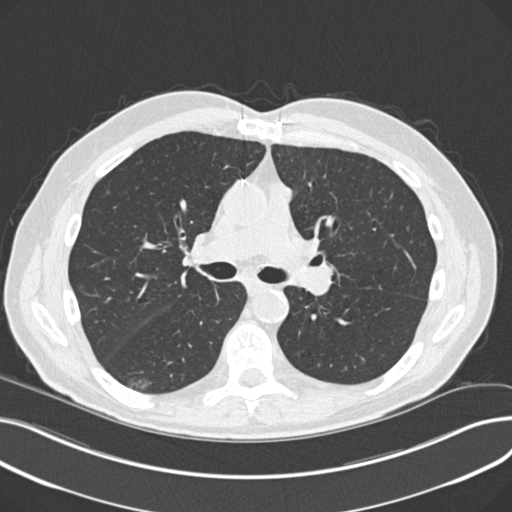
Low-dose screening chest CT, one axial slice; position 130 of 230 along the scan axis; reconstruction kernel B30f; lung window (W 1500 / L -600 HU); 2 mm slice thickness; 512 × 512 image matrix.
Outlined on this slice (manually delineated by an expert):
- lesion 1 (nodule, lower lobe of right lung): bounding box (x1, y1, x2, y2) in pixels: (129, 377, 152, 390)